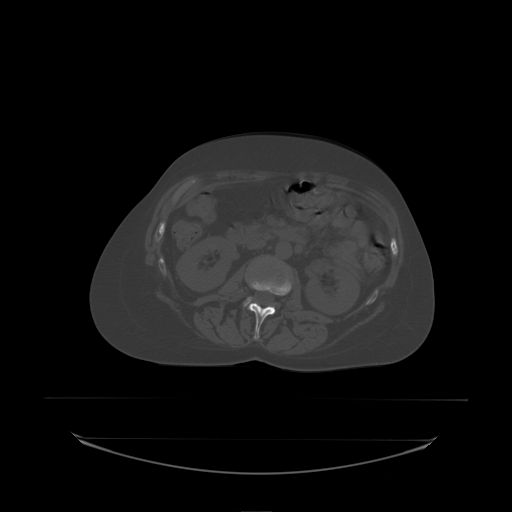
CT including the spine, one axial slice; position 69 of 242 along the scan axis; bone window (W 1800 / L 400 HU); 2.5 mm slice thickness; 512 × 512 image matrix, field of view 500 × 500 mm. Female patient, age 53 years. From the clinical record (not read from this slice): primary cancer: lung; vertebrae with lytic lesions (as recorded): T7, L1.
Structures marked on this image (semi-automatic segmentation, software-assisted and operator-edited):
- L2 vertebra: bounding box (x1, y1, x2, y2) in pixels: (249, 281, 292, 338)
- L3 vertebra: (244, 297, 252, 307)